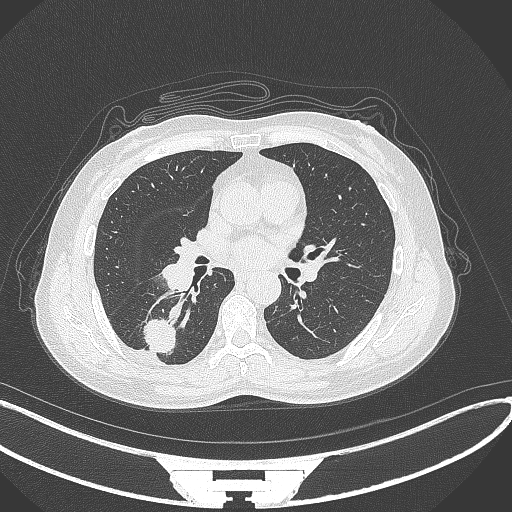
Chest CT, one axial slice. Position 159 of 352 along the scan axis. Reconstruction kernel B70f. Lung window (W 1500 / L -600 HU). 512 × 512 image matrix. Patient: female, 55 years. Case-level facts recorded for this patient, not image findings: clinical TNM (as recorded): T1c N1 M0.
Annotated regions visible in this slice (bounding box drawn by a radiologist):
- lung tumour (recorded histology: adenocarcinoma): bounding box (x1, y1, x2, y2) in pixels: (140, 315, 180, 357)